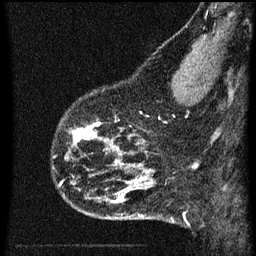
Breast MRI (dynamic contrast-enhanced), one sagittal slice; slice 15 of 60 in the series (ordered by position); dynamic contrast-enhanced series, image 2 of 3 at this slice position (ordered by acquisition); 1.5 T; TE 4.2 ms, TR 8 ms; 2 mm slice thickness; 256 × 256 image matrix, field of view 180 × 180 mm. Female patient, age 43 years.
Outlined on this slice (semi-automatic segmentation, software-assisted and operator-edited):
- analysis volume of interest (the breast-tissue region the enhancement analysis was run in; not a lesion): bounding box <55,106,104,153> (left, top, right, bottom; pixels)
- tumour enhancement mask (voxels above the 70 % enhancement threshold inside the analysis volume of interest): <70,122,104,151>